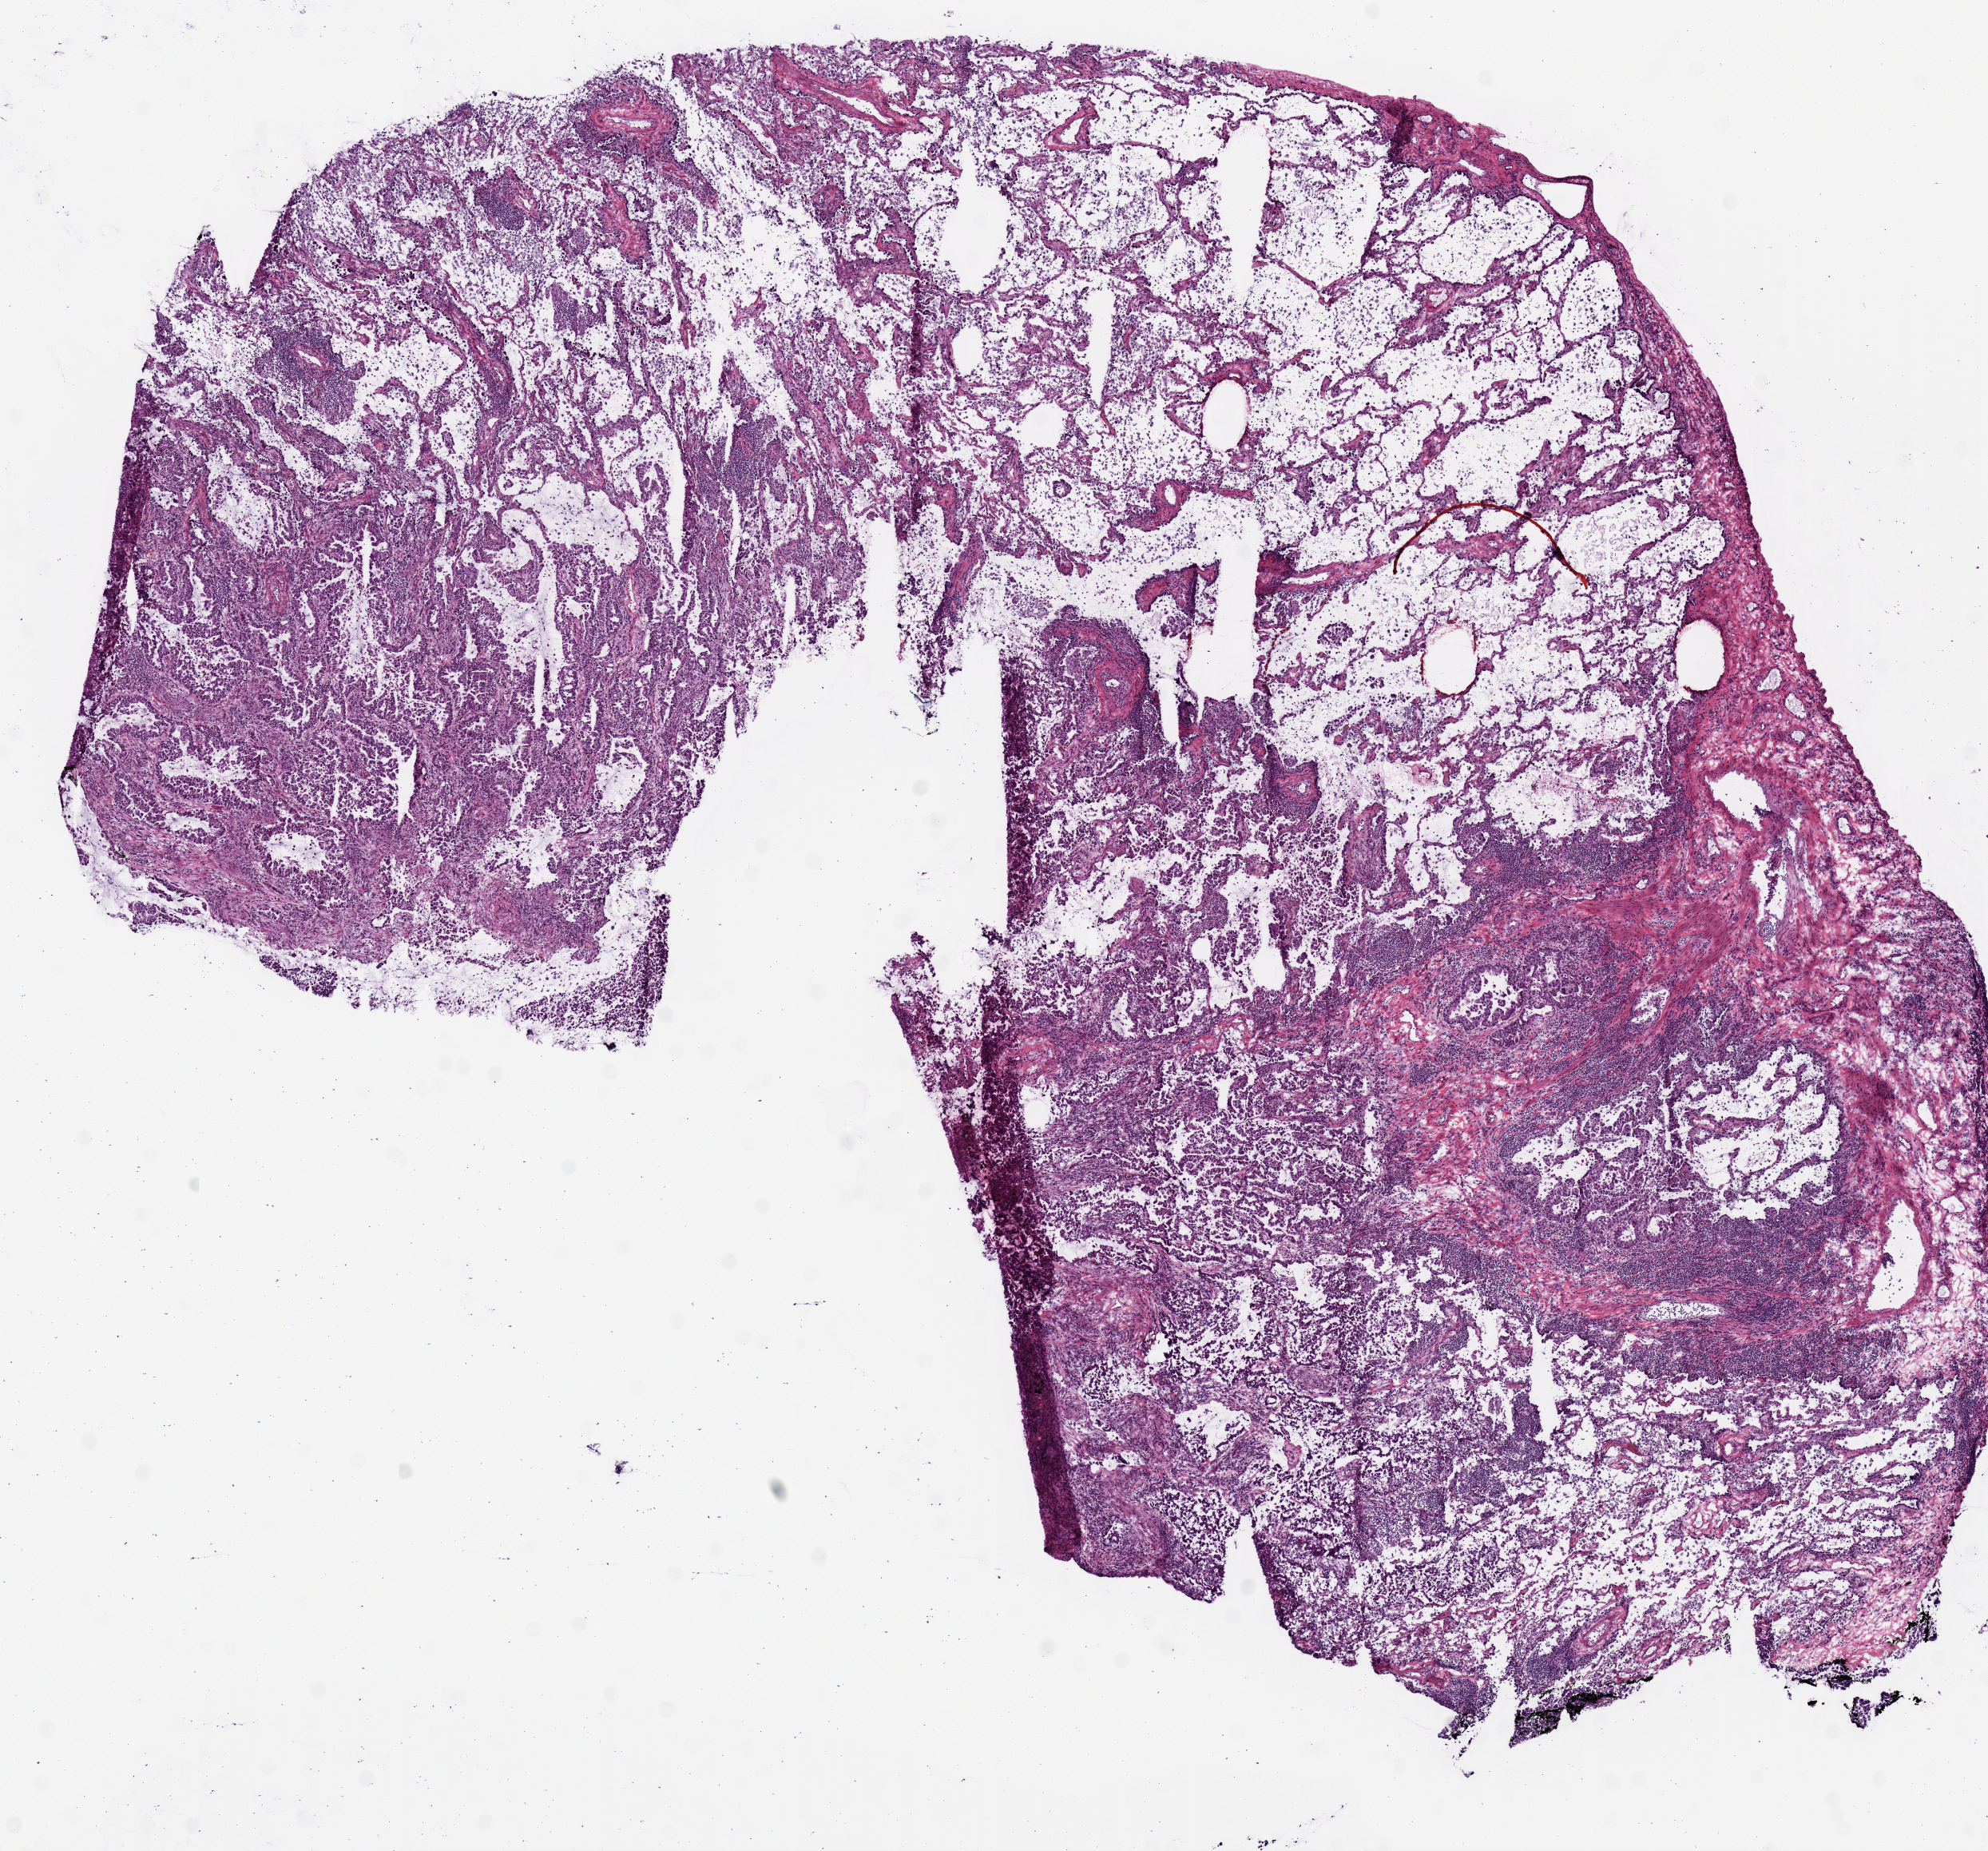
Whole-slide histology image, H&E — a low-resolution overview of the entire scanned area, about 9.8 x 9.2 mm, frozen section, lung, primary tumour sample. Female patient; age at initial diagnosis 69 years. Slide review estimates, as recorded: tumour cells 90%, tumour nuclei 75%, normal cells 0%, stromal cells 10%, necrosis 0%.
Pathologic diagnosis: Adenocarcinoma, NOS (lower lobe, lung). AJCC pathologic stage: IA (7th edition).